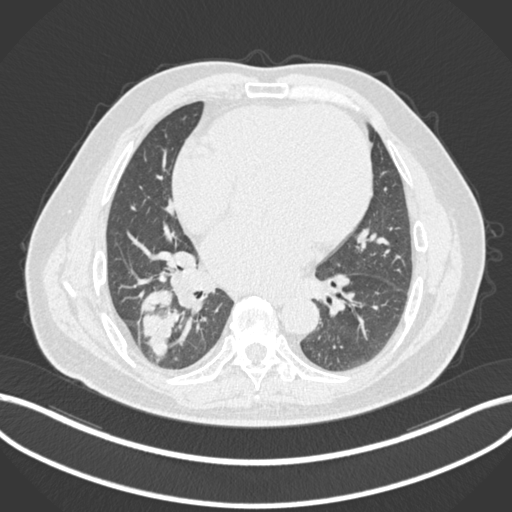
Chest CT, one axial slice; position 78 of 200 along the scan axis; 120 kVp; lung window (W 1500 / L -600 HU); 512 × 512 image matrix, field of view 400 × 400 mm. Male patient, age 59 years.
Annotated regions visible in this slice (bounding box drawn by a radiologist):
- lung tumour (recorded histology: adenocarcinoma): box from (x=135, y=287) to (x=179, y=360) px